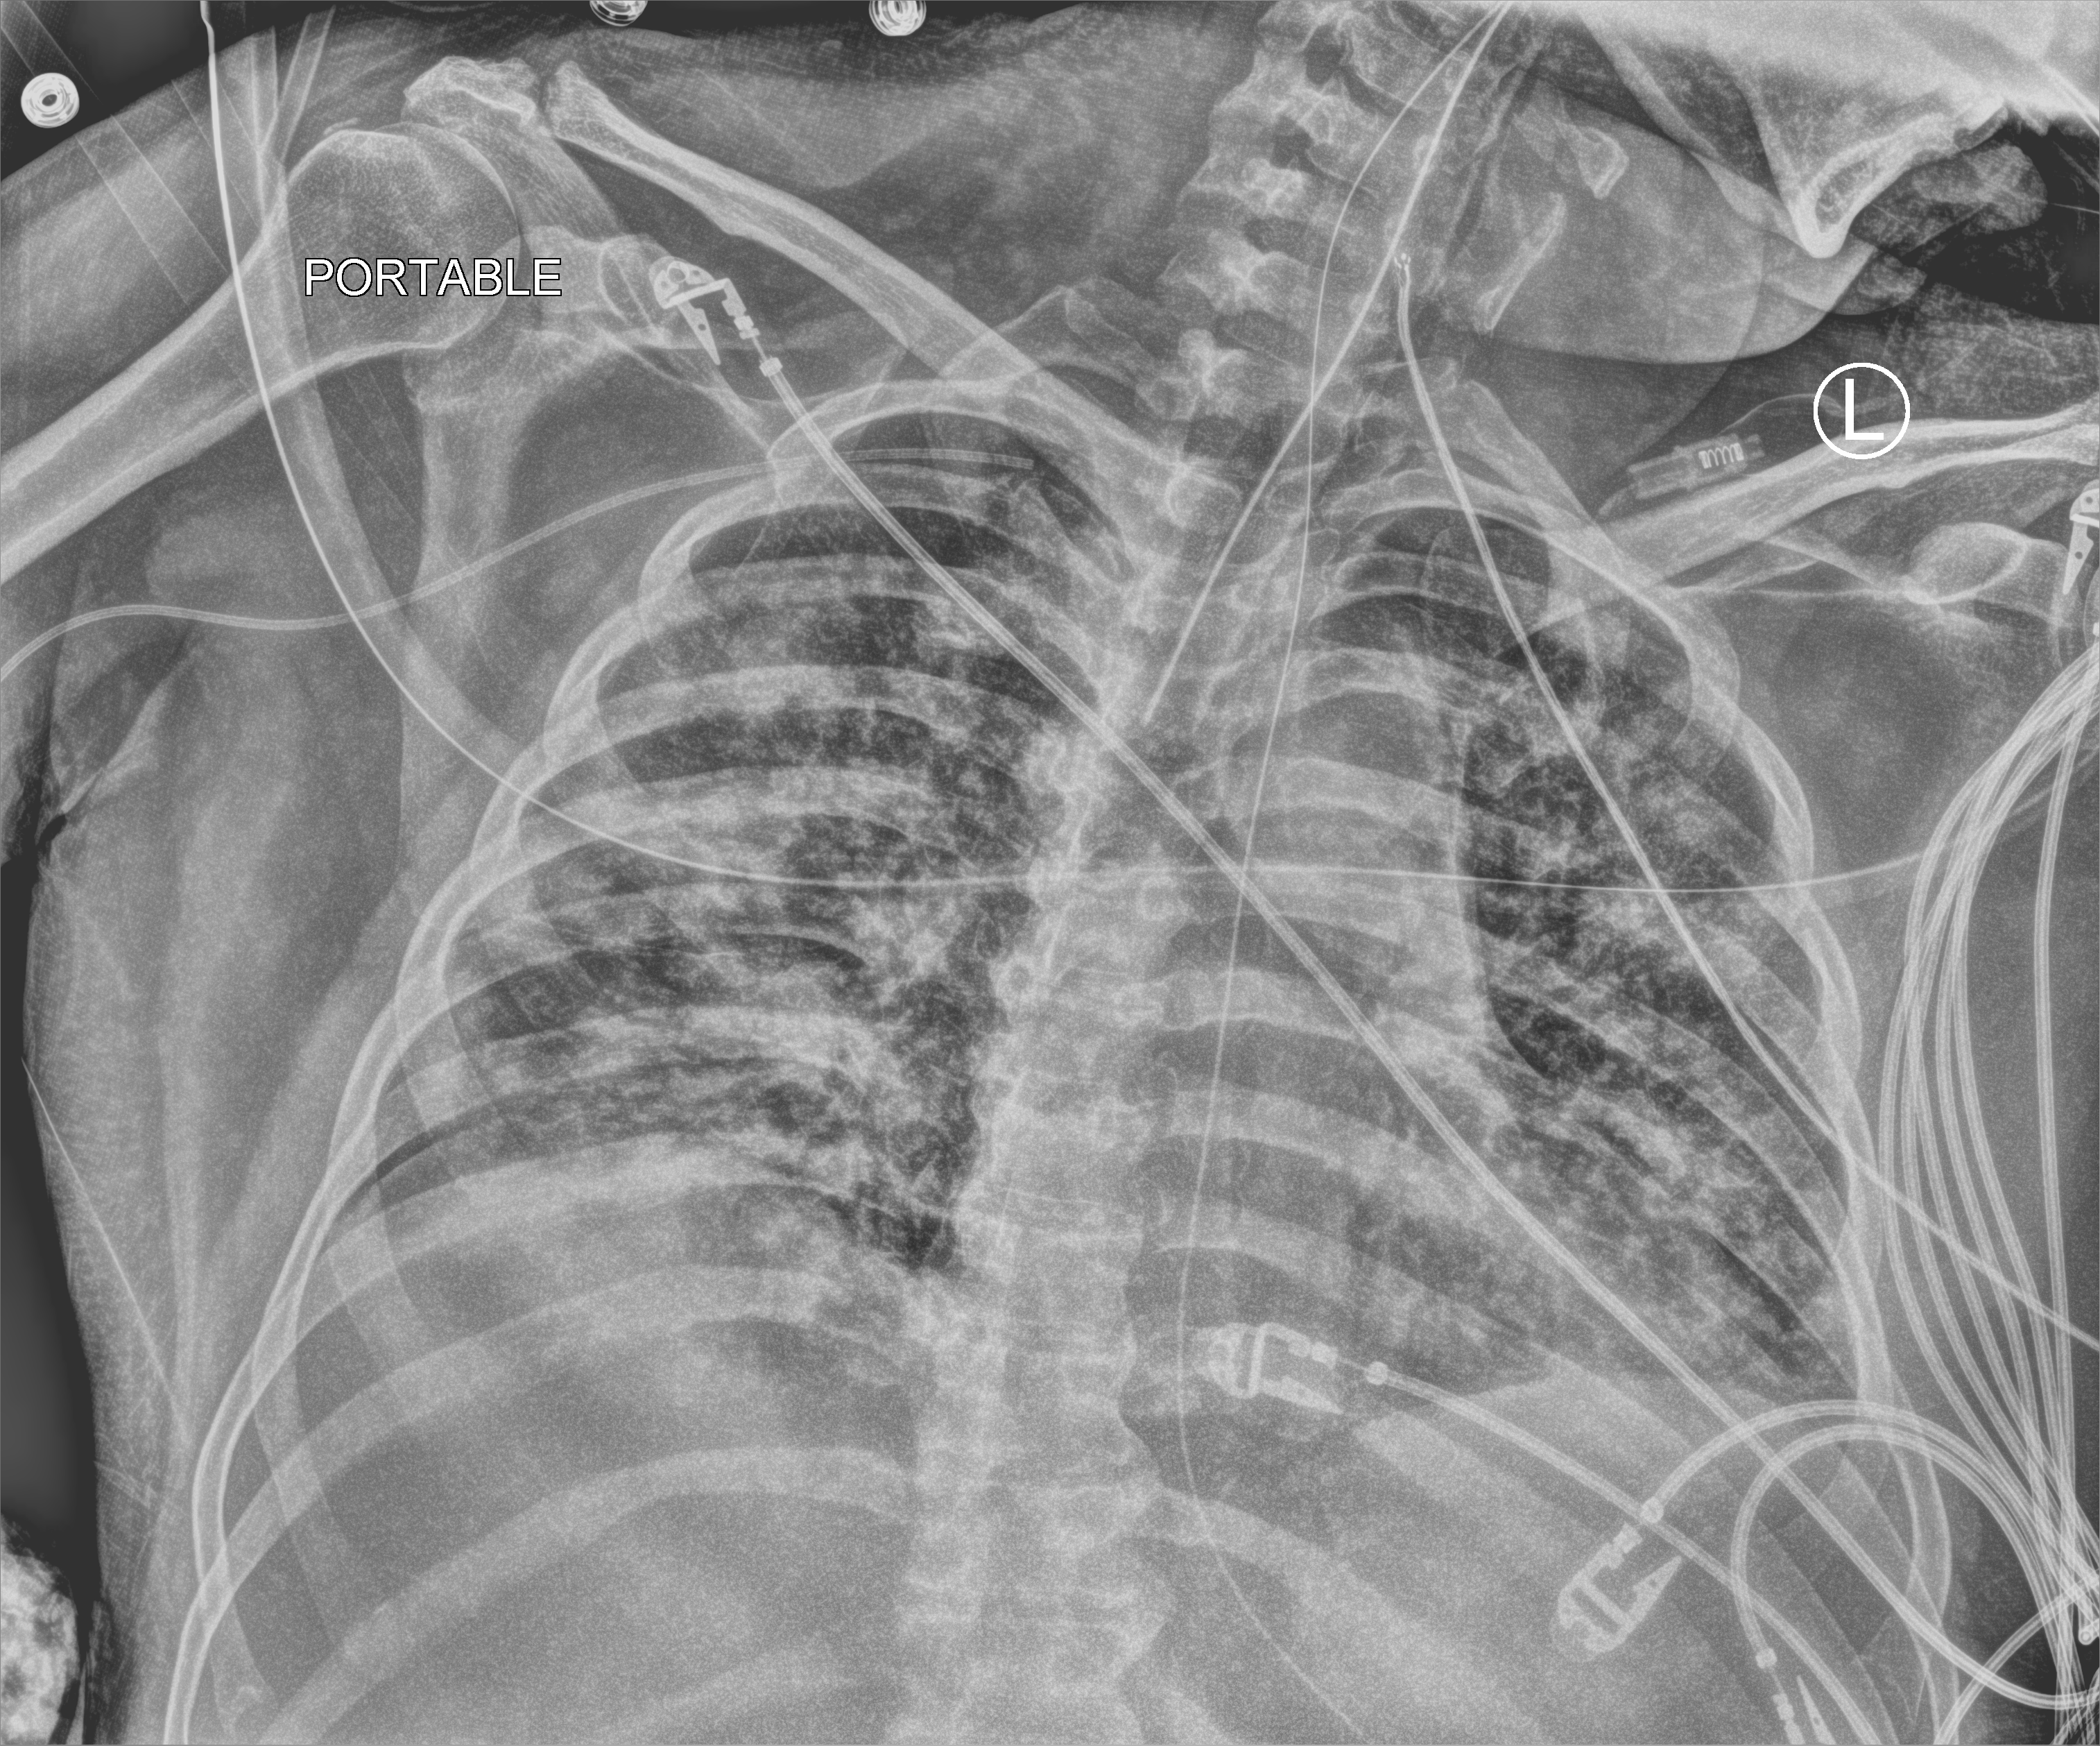
Chest X-ray (portable), anteroposterior (AP) projection. Male patient hospitalised with COVID-19, age 18–59 years.
Hospital-stay facts (about this admission, not read from this image; timing relative to this image not recorded):
- mechanically ventilated during this hospital stay: yes
- admitted to intensive care during this hospital stay: yes
- length of hospital stay: 26 days